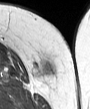
MRI of an extremity soft-tissue mass, one axial slice; position 9 of 45 along the scan axis; MR volume resampled by the dataset authors to the PET/CT grid (not the native acquisition matrix); 3.27 mm slice thickness; 90 × 109 image matrix, field of view 88 × 106 mm. Female patient. From the clinical record (not read from this slice): histological type: leiomyosarcoma; grade: intermediate; site of the primary tumour: parascapusular.
Annotated regions visible in this slice (expert contour drawn on MRI and transferred to this co-registered scan by the dataset authors):
- gross tumour volume including surrounding oedema: bounding box <35,62,56,76> (left, top, right, bottom; pixels)
- gross tumour volume (mass): <42,64,52,74>